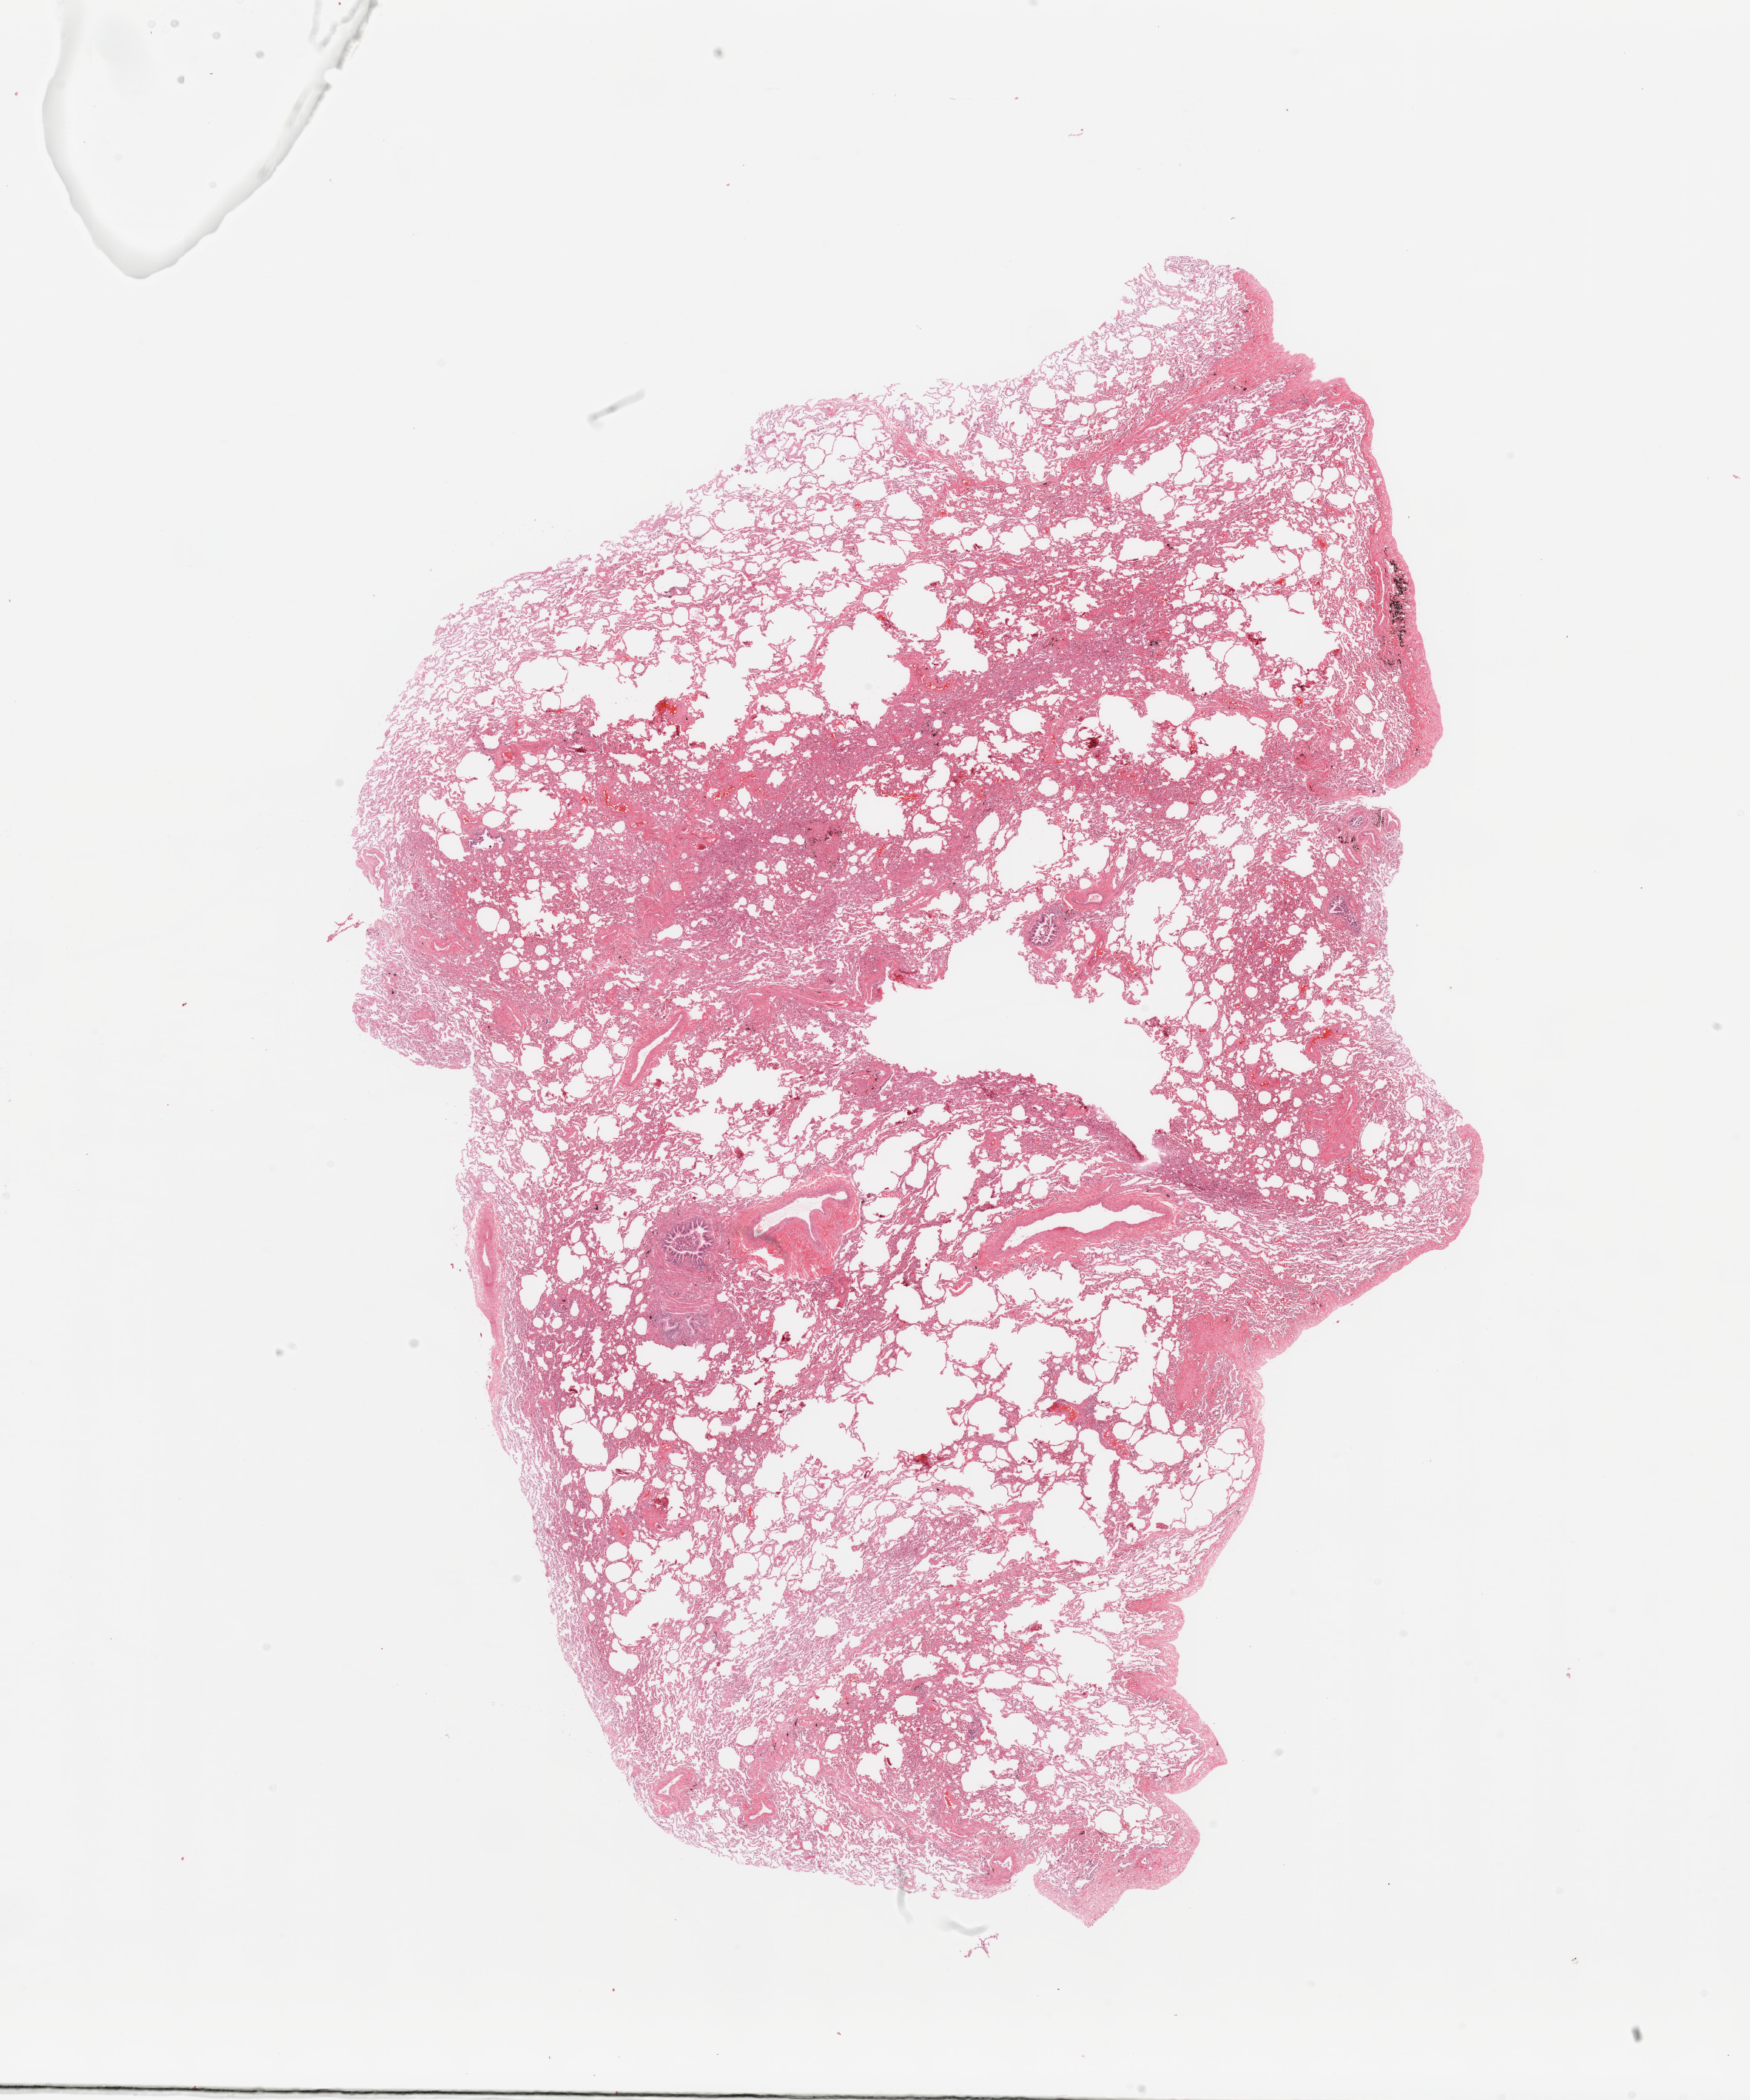
Whole-slide histology image, H&E-stained, low-resolution overview of the scanned area, about 18.7 x 22.4 mm (acquisition: 20x scan); normal (non-tumour) tissue sample, sampled site: lung. Female, 49 y/o.
This section: normal (non-tumour) tissue from the same patient. Patient diagnosis: Adenocarcinoma, NOS.